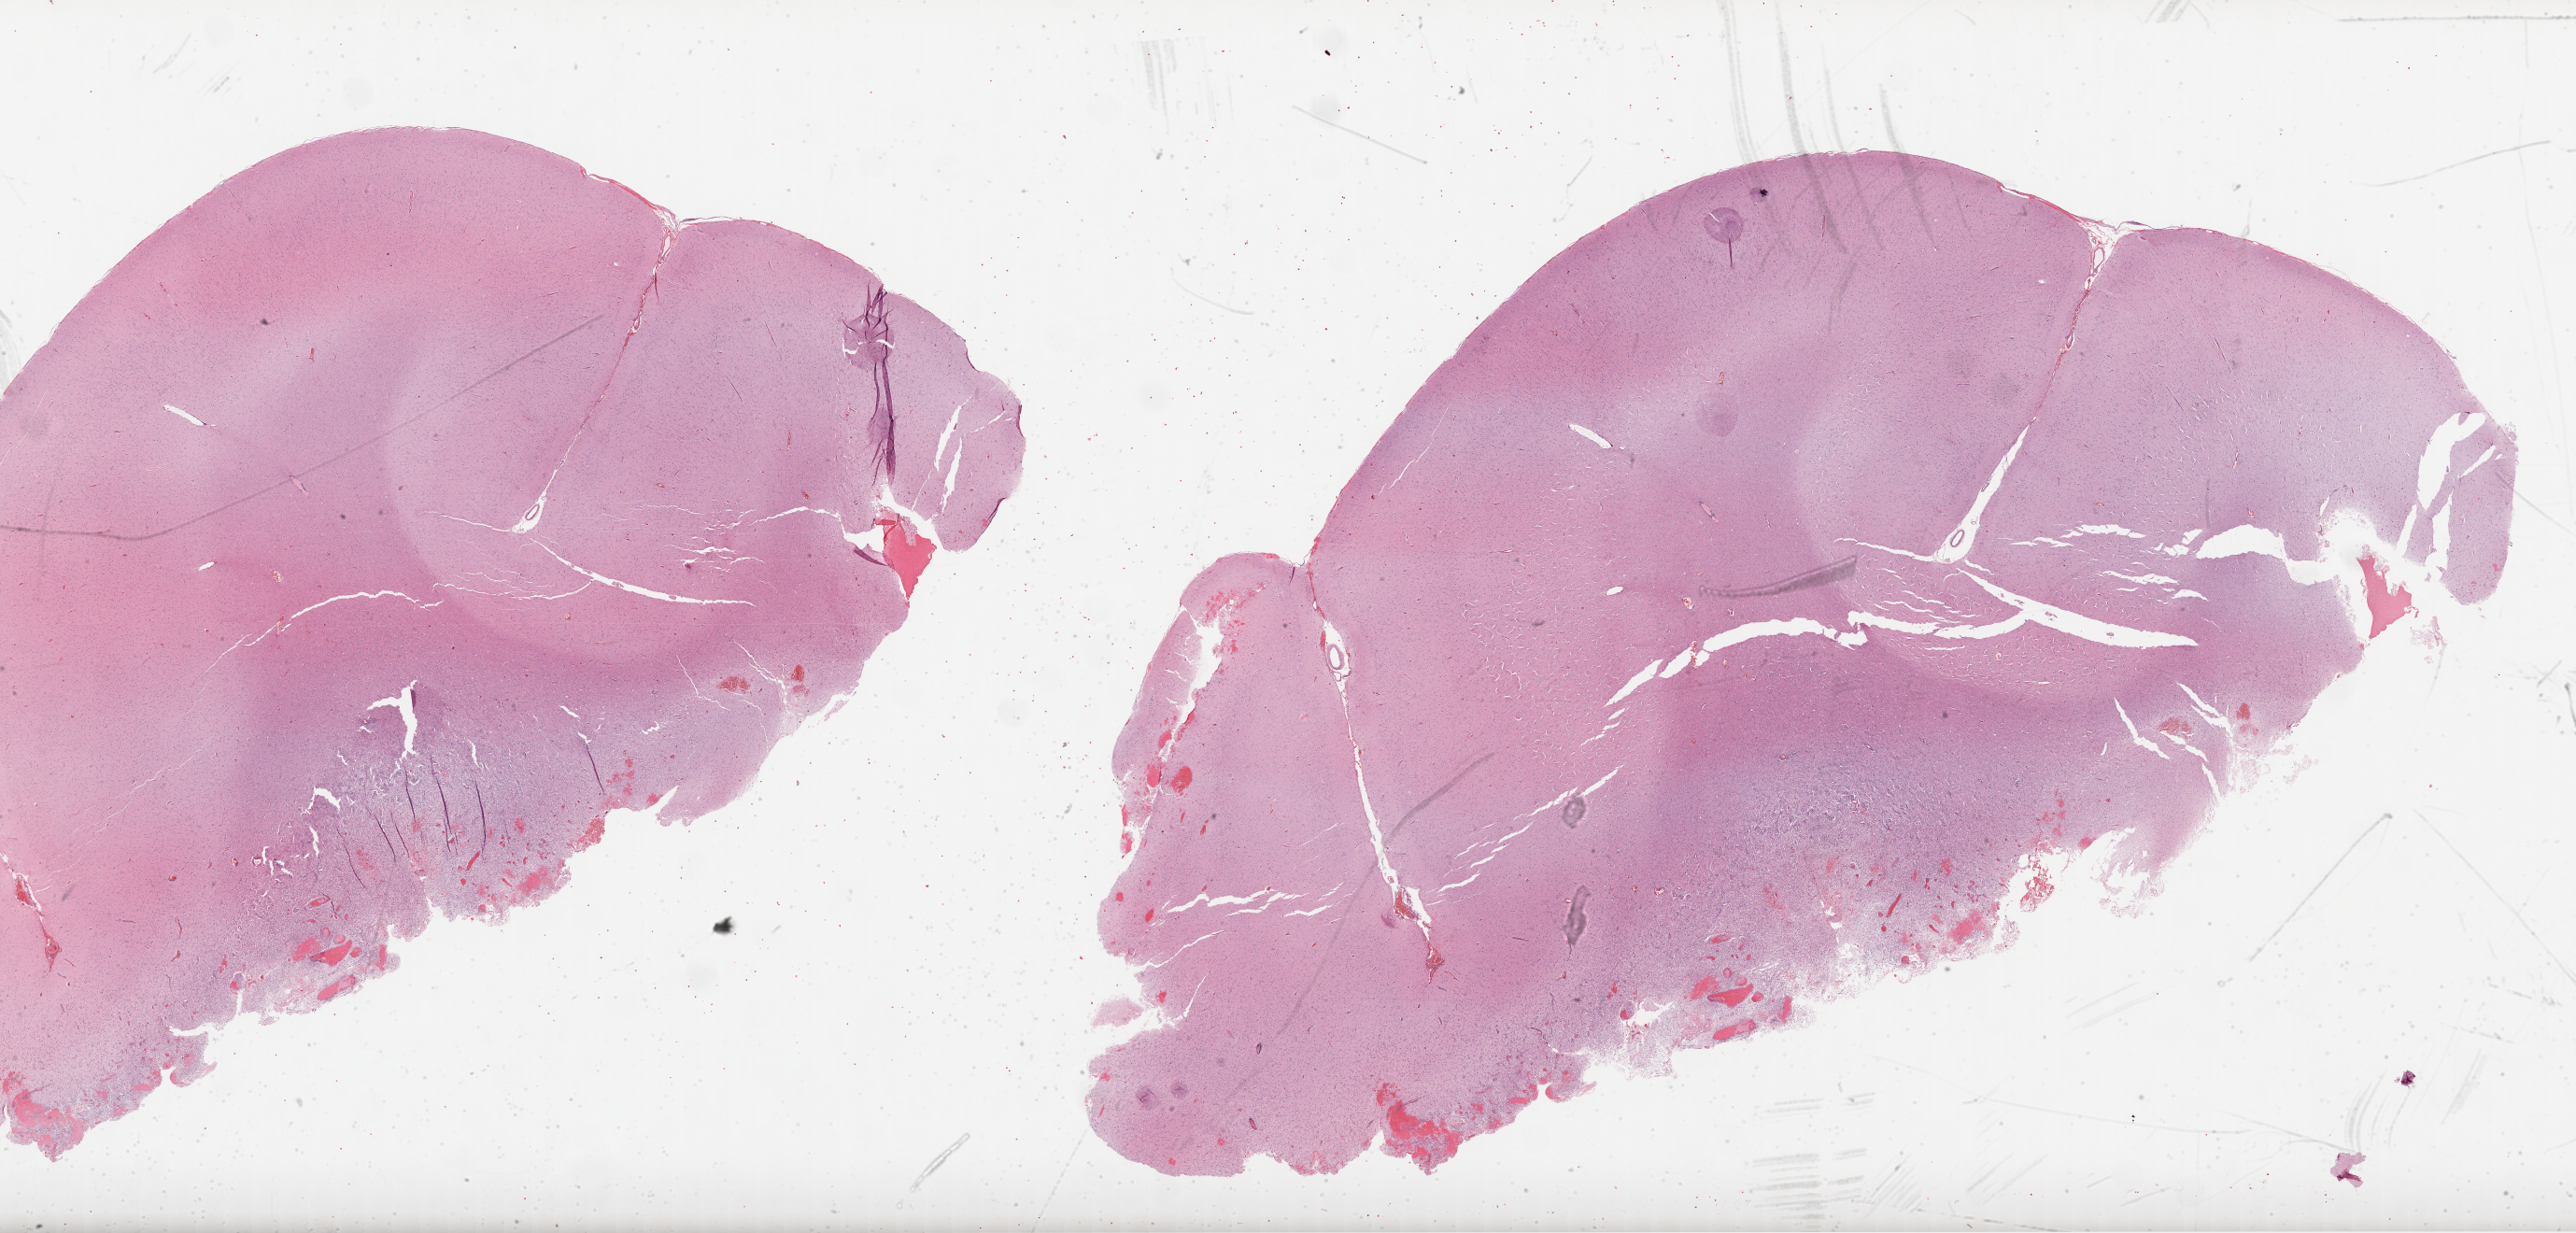
Digitized H&E tissue section (whole slide) — whole scanned area (about 44.5 x 21.3 mm, slide scanned at 20x) shown as a low-resolution overview; formalin-fixed paraffin-embedded (FFPE) diagnostic section; brain, primary tumour sample. Male, age 54 years at initial diagnosis.
Histologic diagnosis: Glioblastoma.